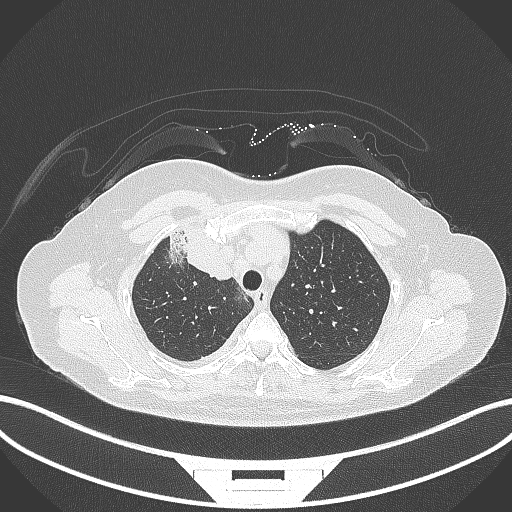
Chest CT, one axial slice. Slice 243 of 305 in the series (ordered by position). Reconstruction kernel B70f. 120 kVp. Lung window (W 1500 / L -600 HU). 1 mm slice thickness. 512 × 512 image matrix, field of view 400 × 400 mm. Patient: female, 52 years. Case-level facts recorded for this patient, not image findings: clinical TNM (as recorded): T3 N1 M1.
Outlined on this slice (rectangle marked by the reading radiologist):
- lung tumour (recorded histology: adenocarcinoma): bounding box [x1, y1, x2, y2] px = [165, 226, 236, 283]